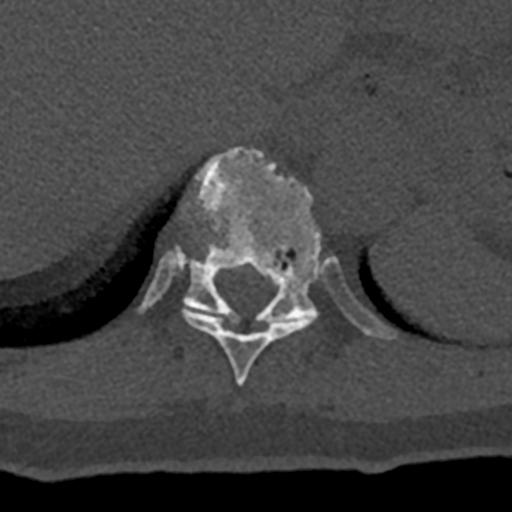
CT including the spine, one axial slice; position 577 of 797 along the scan axis; reconstruction kernel Br40s/3; 120 kVp; bone window (W 1800 / L 400 HU); 0.5 mm slice thickness; 512 × 512 image matrix. Male patient, age 74 years. From the clinical record (not read from this slice): primary cancer: renal.
Outlined on this slice (semi-automatically segmented with operator editing):
- T10 vertebra: bounding box (x1, y1, x2, y2) in pixels: (182, 305, 312, 385)
- T11 vertebra: (139, 147, 396, 340)